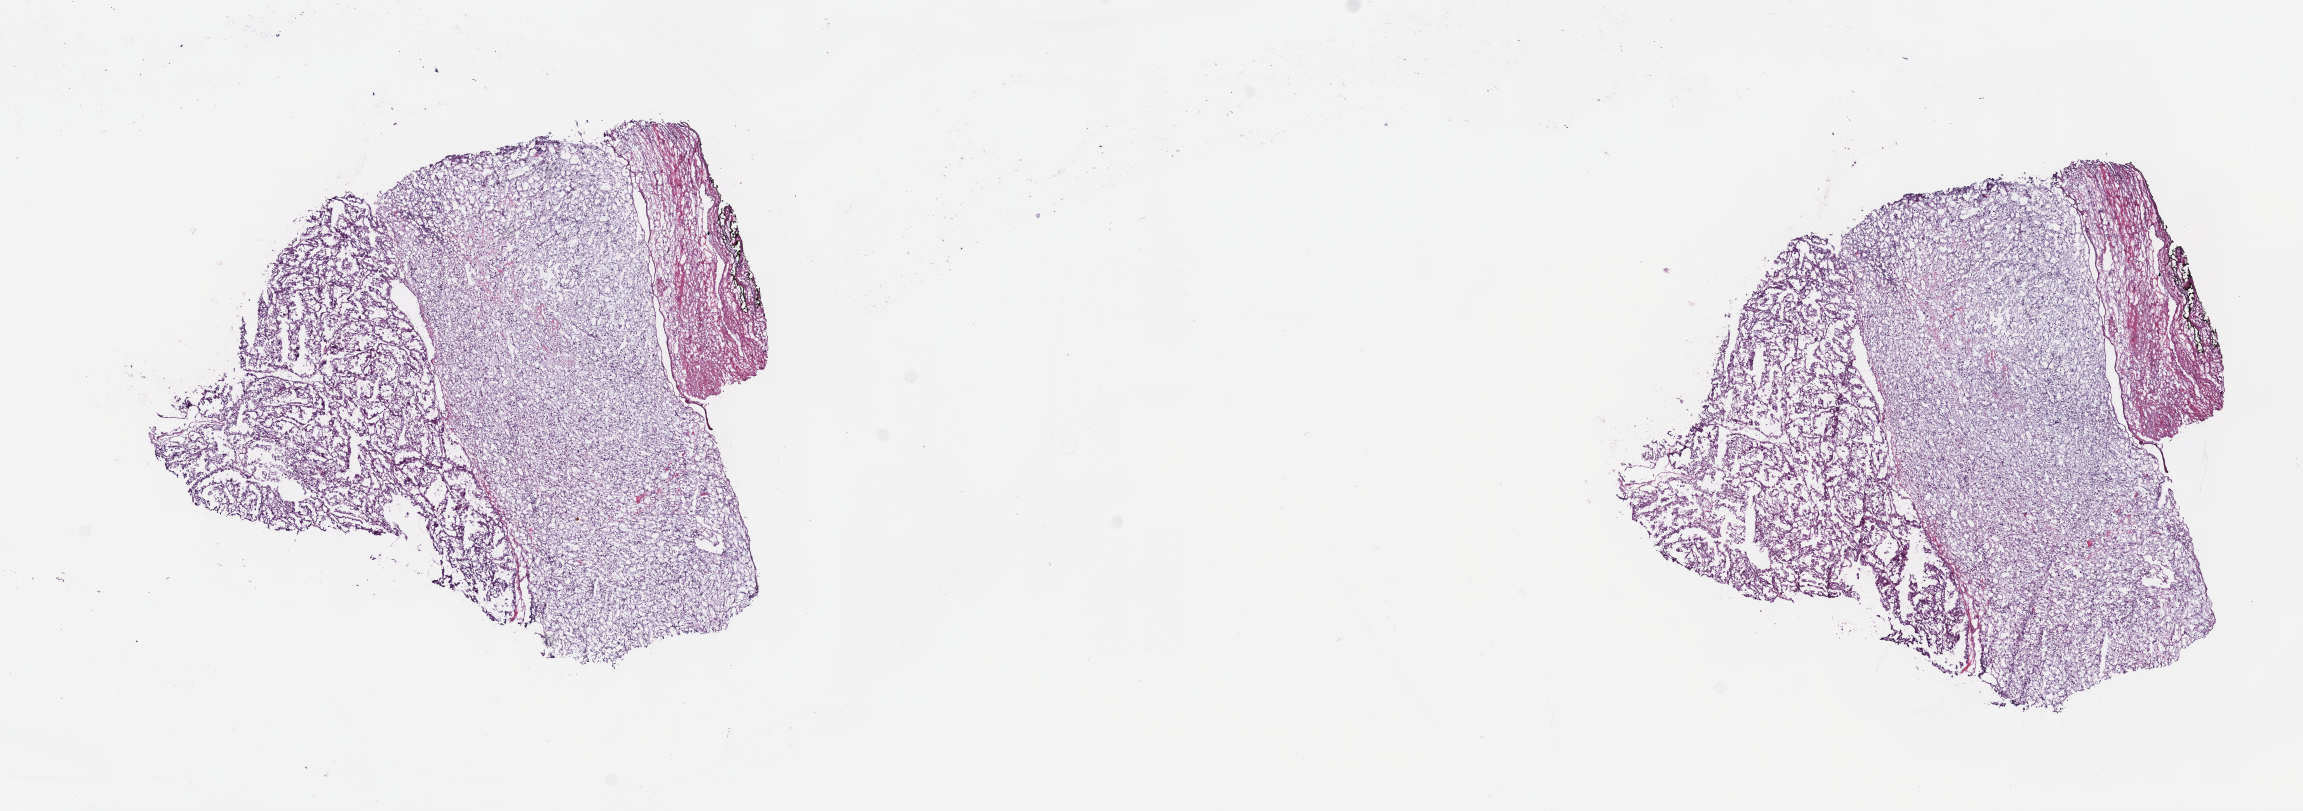
Whole-slide histology image, Hematoxylin and eosin (H&E) stained — a low-resolution overview of the entire scanned area, about 18.6 x 6.6 mm (acquisition: 40x scan); frozen section from the top of the tissue portion; primary tumour sample from the kidney. Patient: female, age at initial diagnosis 58 years. Histologic grade: G2 (moderately differentiated). Pathologist review of this section (percent, as recorded): tumour cells 100%, tumour nuclei 80%, normal cells 0%, stromal cells 0%, necrosis 0%. Infiltration values recorded for this section: lymphocyte infiltration 2%, monocyte infiltration 2%, neutrophil infiltration 0%.
- diagnosis: Clear cell adenocarcinoma, NOS
- laterality: bilateral
- AJCC pathologic stage: I